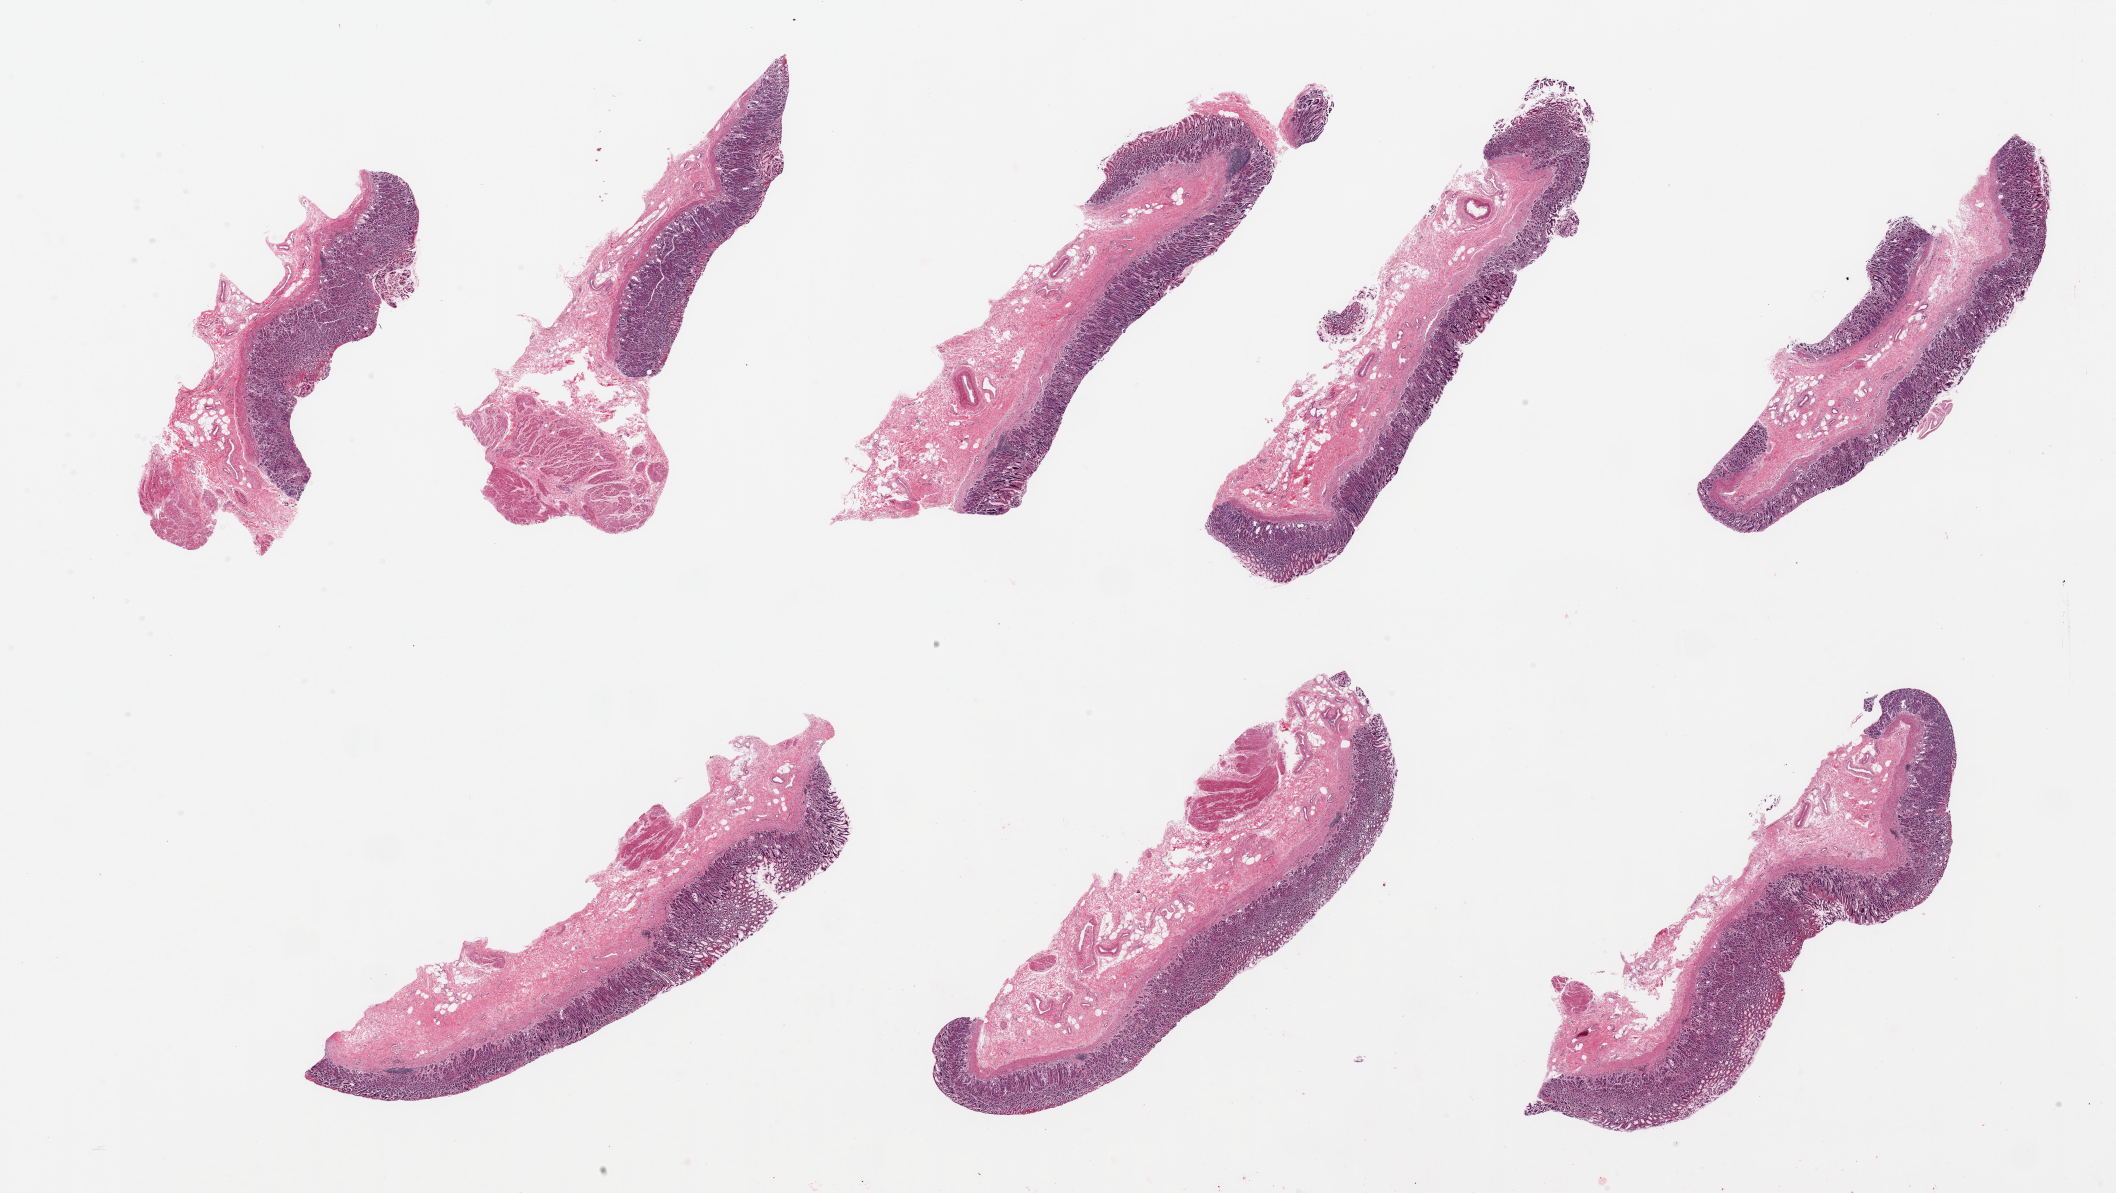
Whole-slide image, hematoxylin and eosin (H&E) stain, low-resolution overview of the scanned area, about 33.5 x 18.9 mm. PAXgene-fixed, paraffin-embedded tissue. Section of stomach (target tissue). Donor tissue sample. Male donor.
* review note (as recorded): 8 pieces; variable representation of mucosa, submucosa, and muscularis; dilated deep glands, moderate acute gastritis